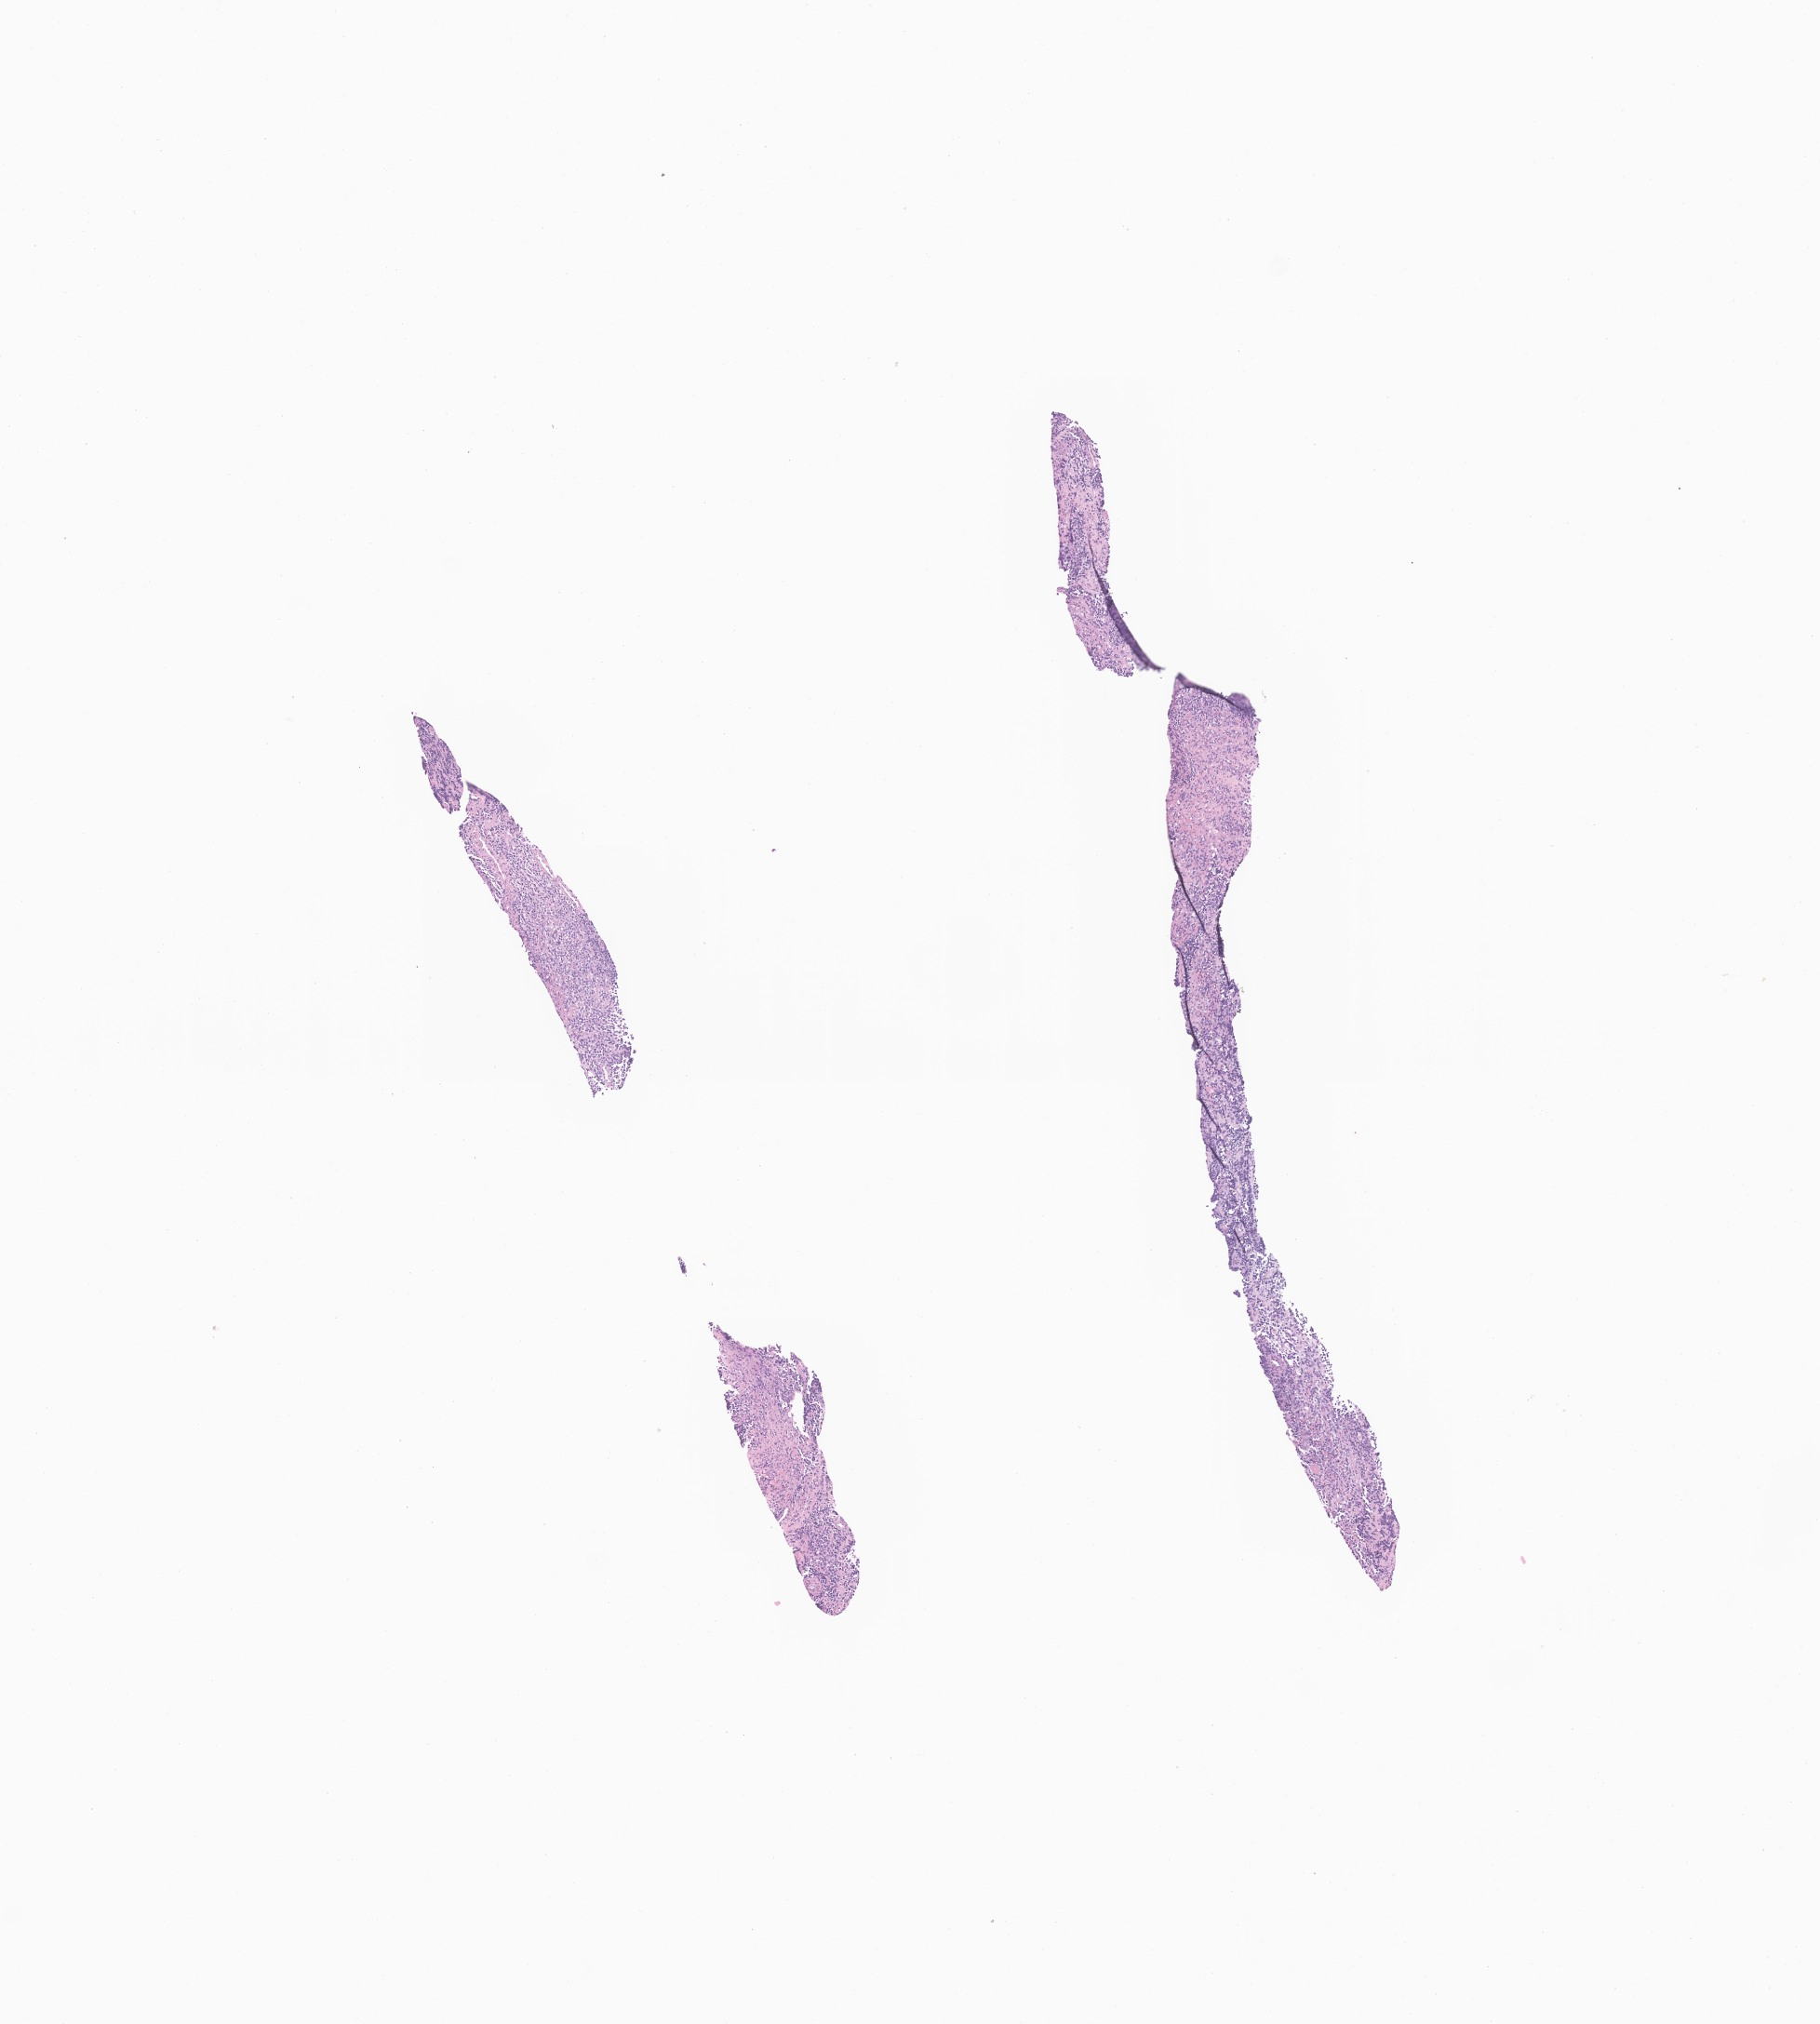
Digitized haematoxylin and eosin-stained section of tumor tissue from the soft tissue, shown as a low-resolution overview of the whole scanned area (about 8.2 x 9.2 mm), FFPE section. Patient female; age 90 months (7 years 6 months).
Diagnosis (ICD-O-3 morphology term): Rhabdomyosarcoma, NOS.